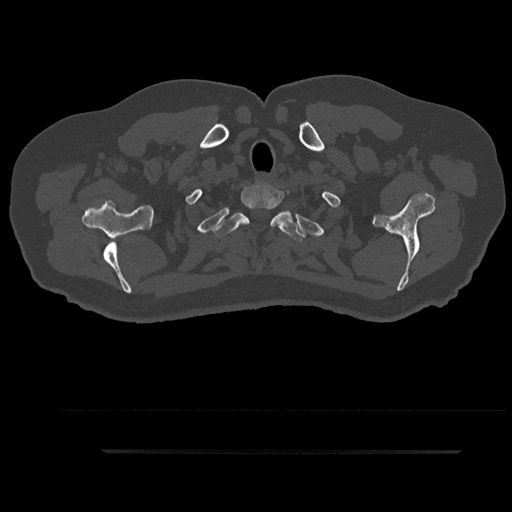
CT including the spine, one axial slice. Slice 778 of 797 in the series (ordered by position). Reconstruction kernel Br40s/3. 120 kVp. Bone window (W 1800 / L 400 HU). 512 × 512 image matrix, field of view 432 × 432 mm. Male patient, age 63 years. Case-level facts recorded for this patient, not image findings: primary cancer: renal.
Outlined on this slice (semi-automatic segmentation, software-assisted and operator-edited):
- T1 vertebra: bounding box <241,185,291,225> (left, top, right, bottom; pixels)
- T2 vertebra: <213,206,306,241>